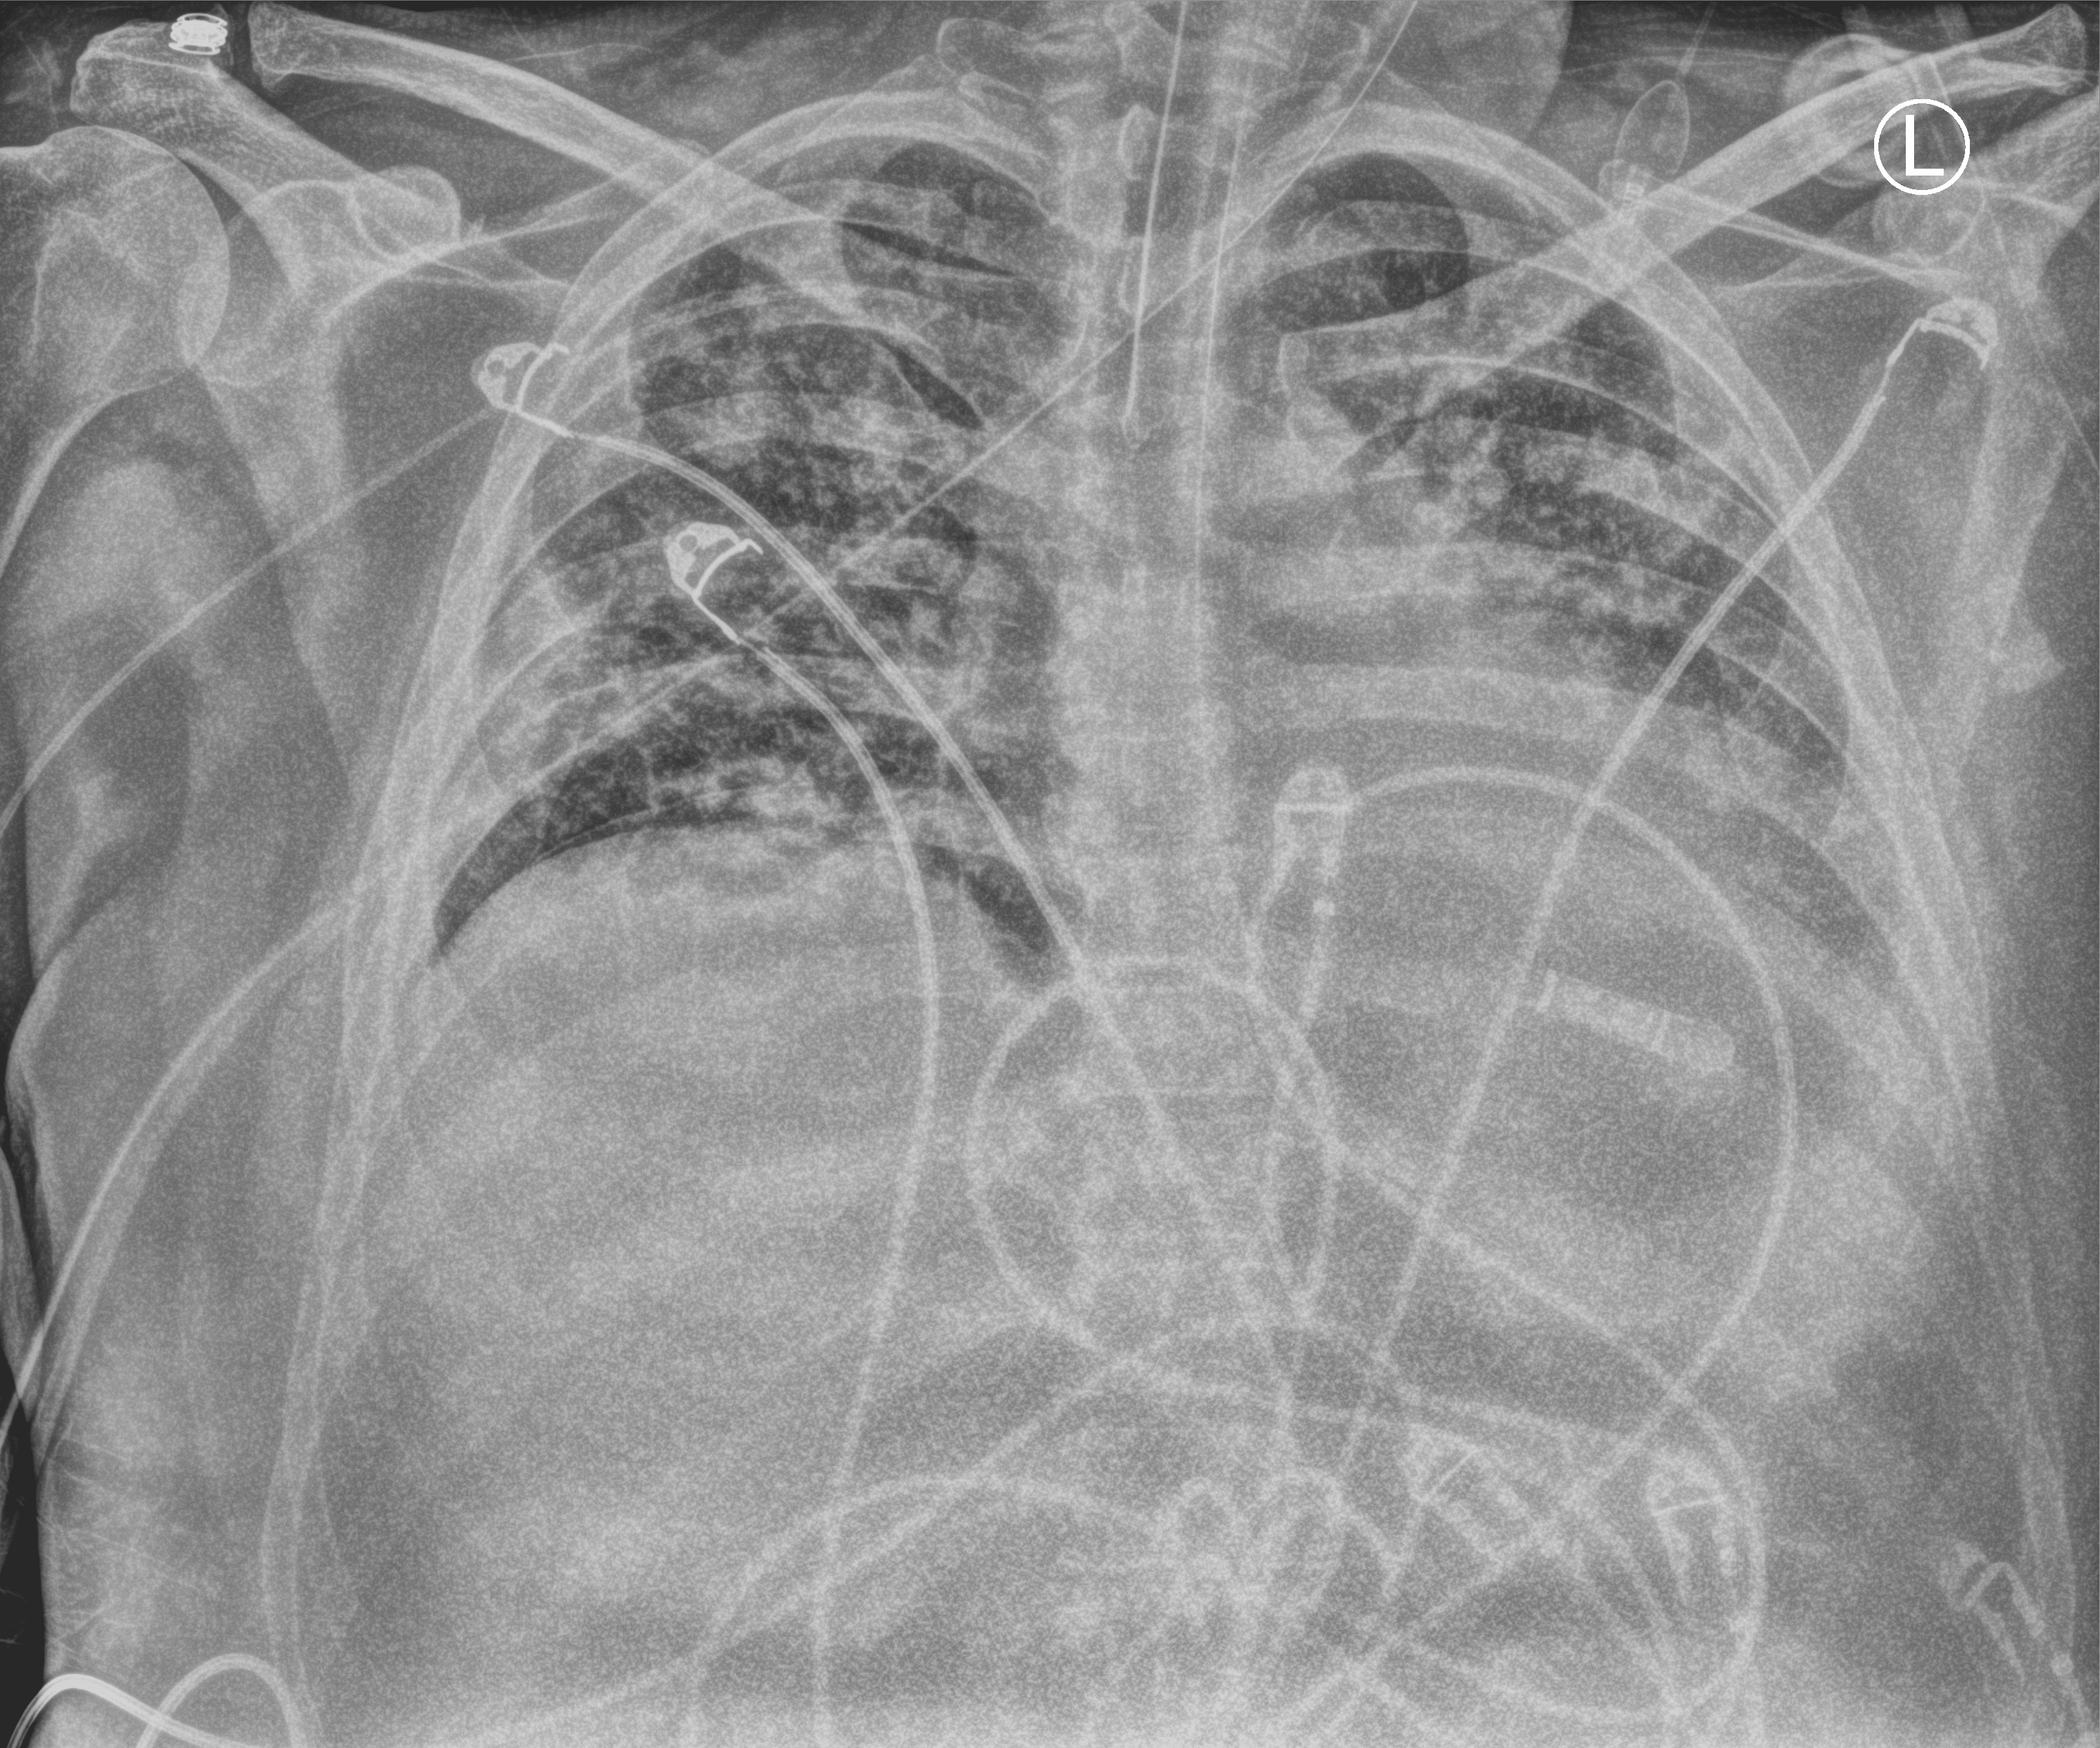
Chest X-ray (portable), anteroposterior (AP) projection. Male patient hospitalised with COVID-19, age 18–59 years.
From the hospital-stay record, not from the radiograph (when in the stay this image was taken is not recorded): length of hospital stay: 39 days.